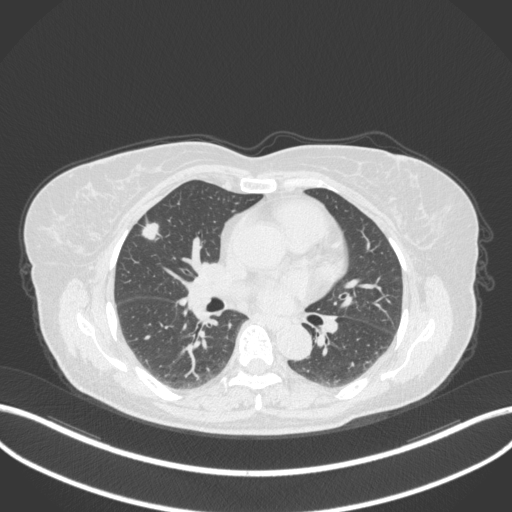
Chest CT, one axial slice. Position 177 of 310 along the scan axis. Reconstruction kernel B31f. 120 kVp. Lung window (W 1500 / L -600 HU). 512 × 512 image matrix, field of view 400 × 400 mm. Female patient, age 55 years. From the clinical record (not read from this slice): clinical TNM (as recorded): T1b N0 M0; histopathological grade: G2.
Structures marked on this image (bounding box drawn by a radiologist):
- lung tumour (recorded histology: adenocarcinoma): bounding box [x1, y1, x2, y2] px = [139, 215, 160, 243]